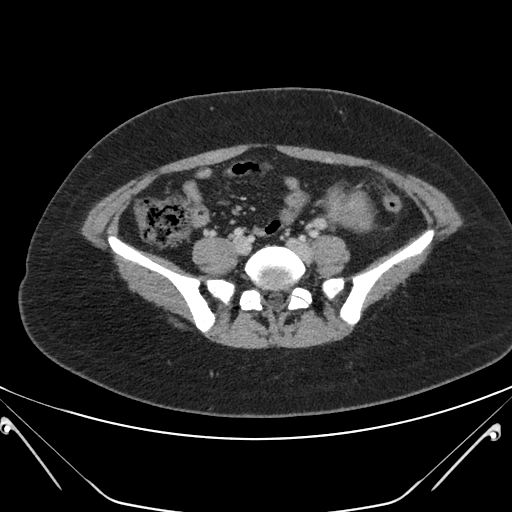
Contrast-enhanced abdominal CT, one axial slice. Slice 64 of 168 in the series (ordered by position). Intravenous contrast given. Soft-tissue window (W 400 / L 40 HU). 3 mm slice thickness. 512 × 512 image matrix, field of view 394 × 394 mm. Female patient, age 26 years. Case-level facts recorded for this patient, not image findings: diagnosis: adrenocortical carcinoma; tumour side: left adrenal; tumour size at pathology: 28 cm; Ki-67 index: 20 %; stage (as recorded): 2.
Structures marked on this image (semi-automatic segmentation, software-assisted and operator-edited):
- mass: bounding box (x1, y1, x2, y2) in pixels: (333, 197, 369, 224)